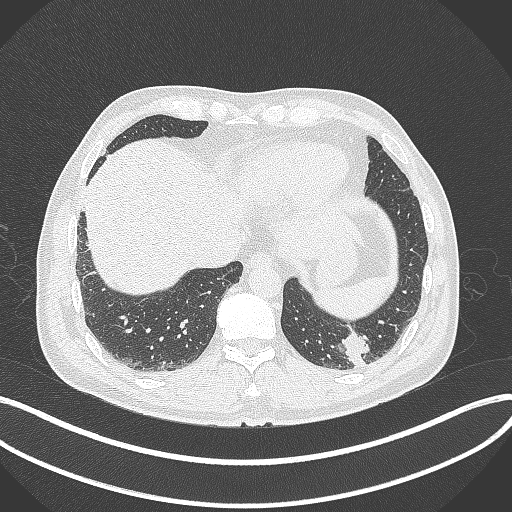
Chest CT, one axial slice; 120 kVp; lung window (W 1500 / L -600 HU); 1 mm slice thickness; 512 × 512 image matrix, field of view 400 × 400 mm. Patient: male, 54 years. Case-level facts recorded for this patient, not image findings: clinical TNM (as recorded): T1c N0 M1; histopathological grade: G3.
Outlined on this slice (bounding box drawn by a radiologist):
- lung tumour (recorded histology: adenocarcinoma): bounding box (x1, y1, x2, y2) in pixels: (340, 330, 369, 371)